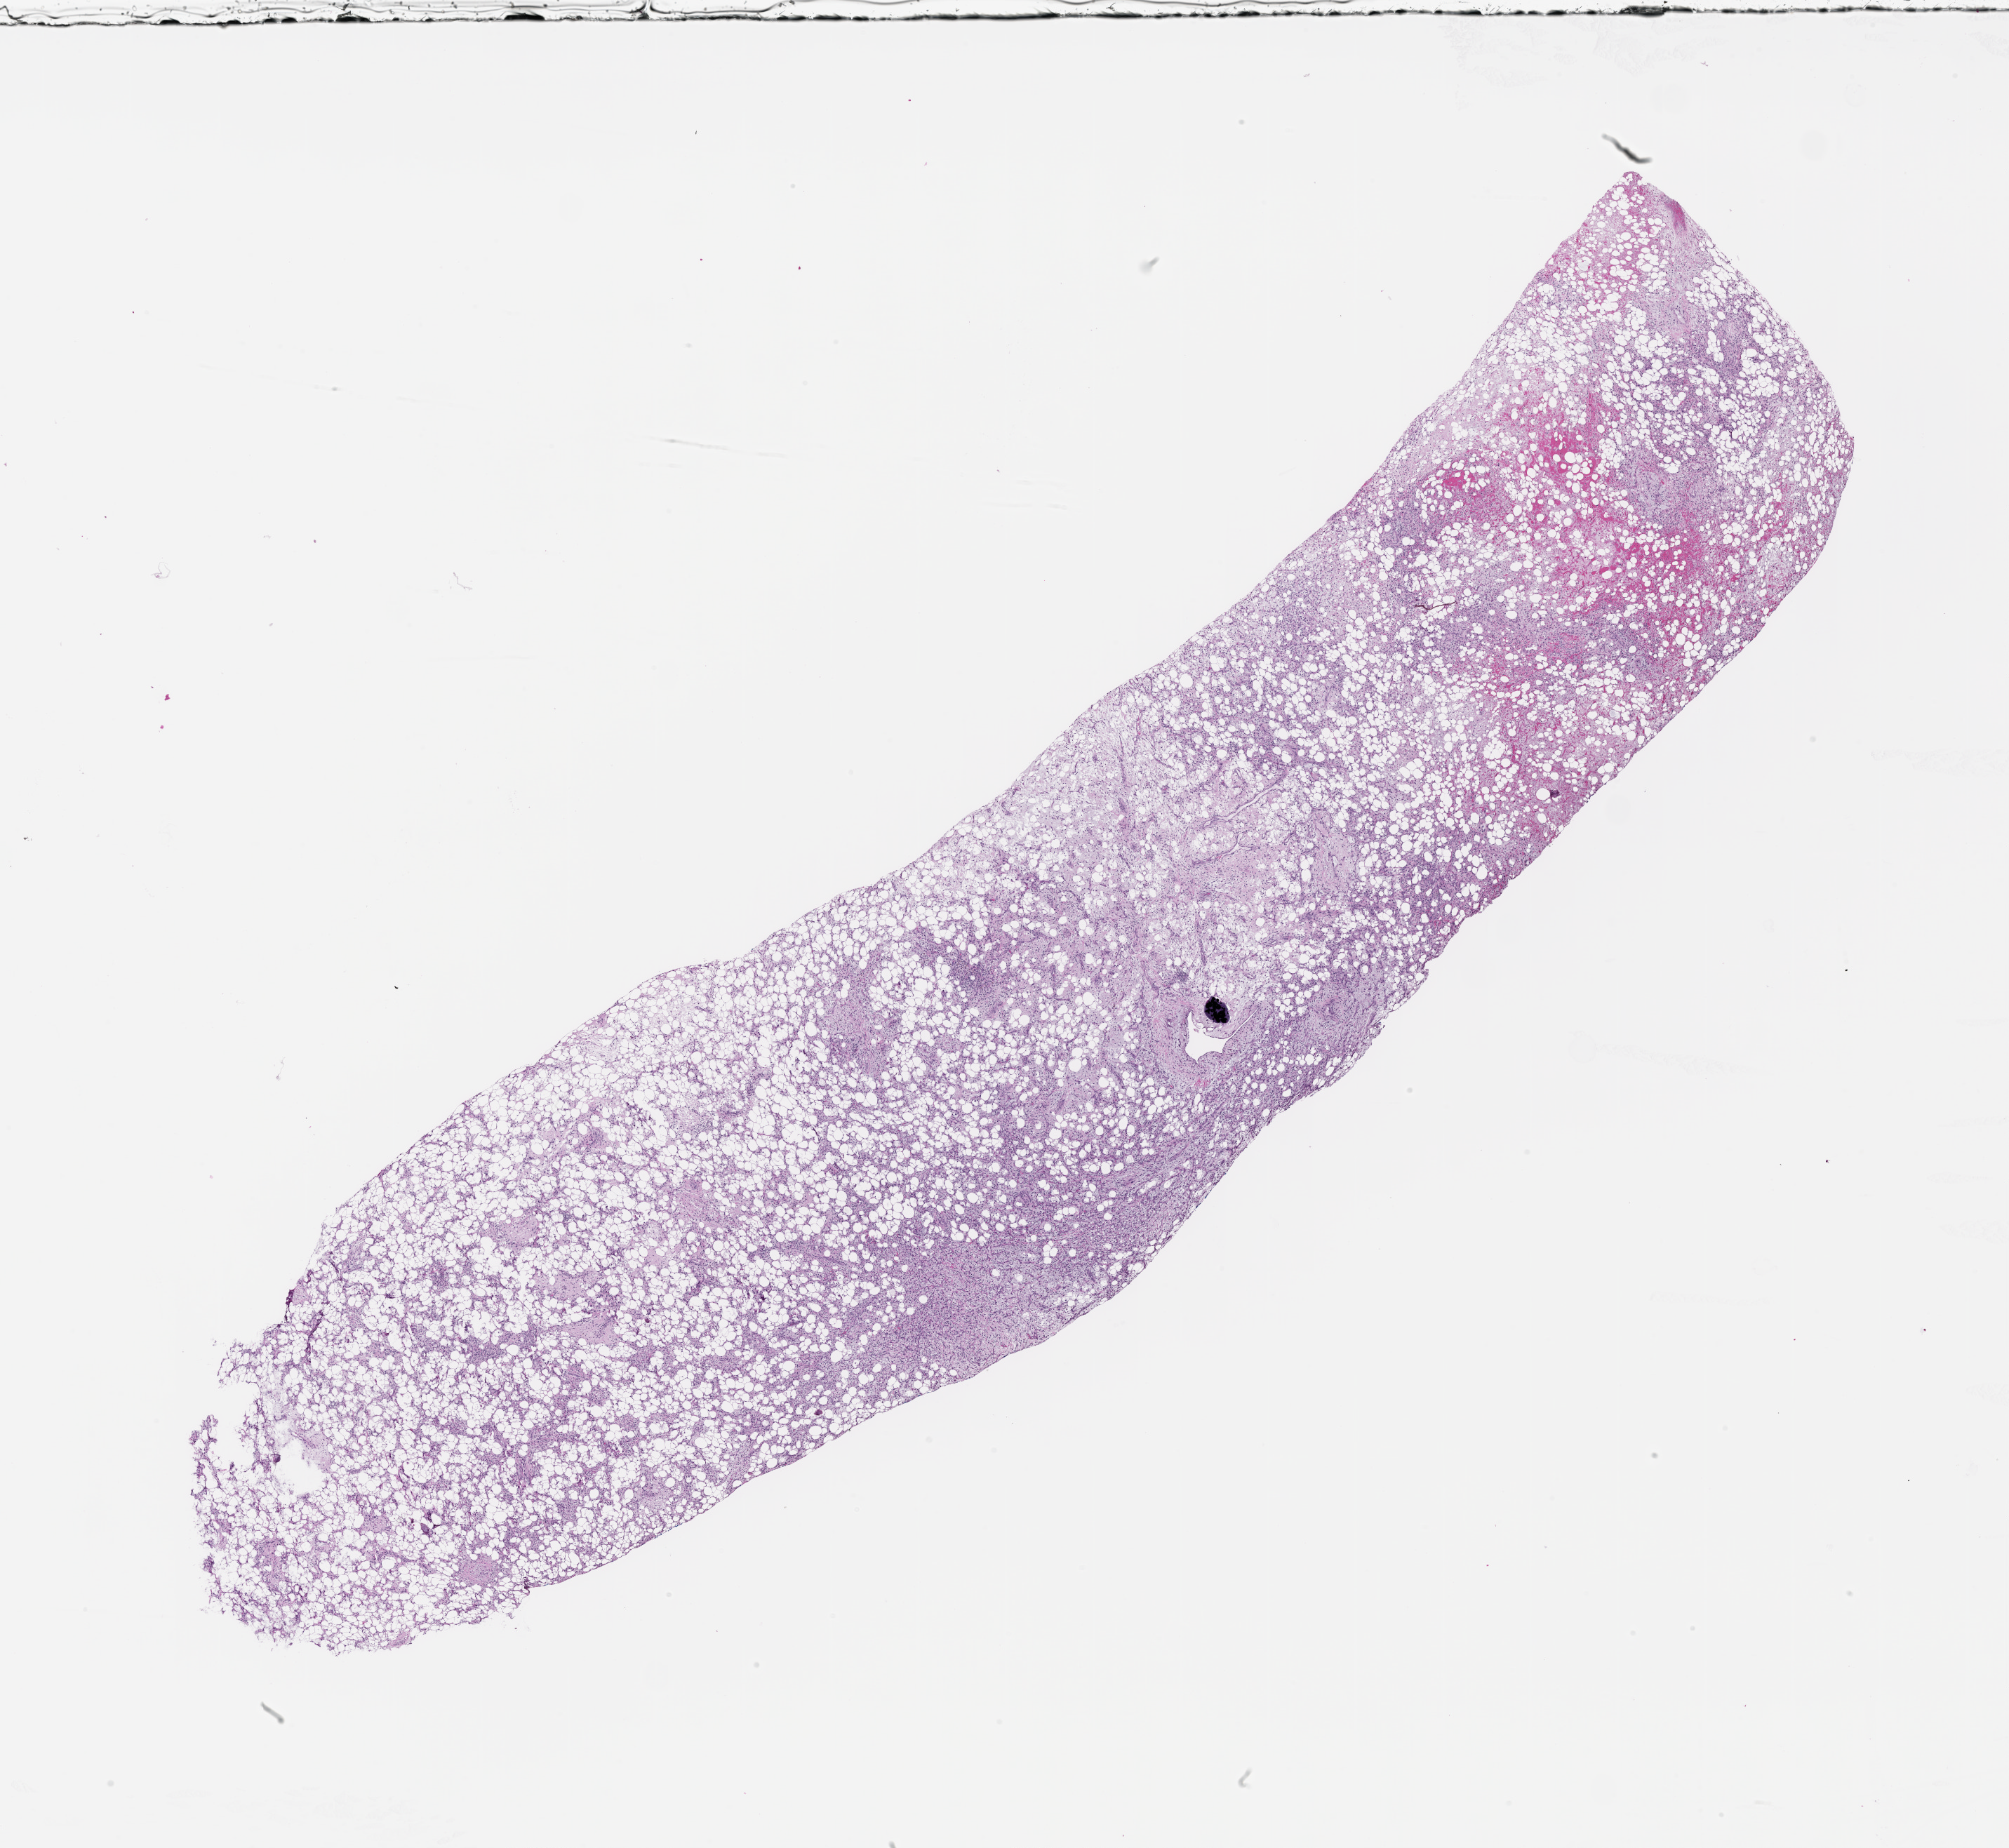
Whole-slide histology image, H&E — a low-resolution overview of the entire scanned area, about 23.1 x 21.2 mm.
Patient diagnosis (cohort enrolment): sarcoma (site not recorded at cohort level).